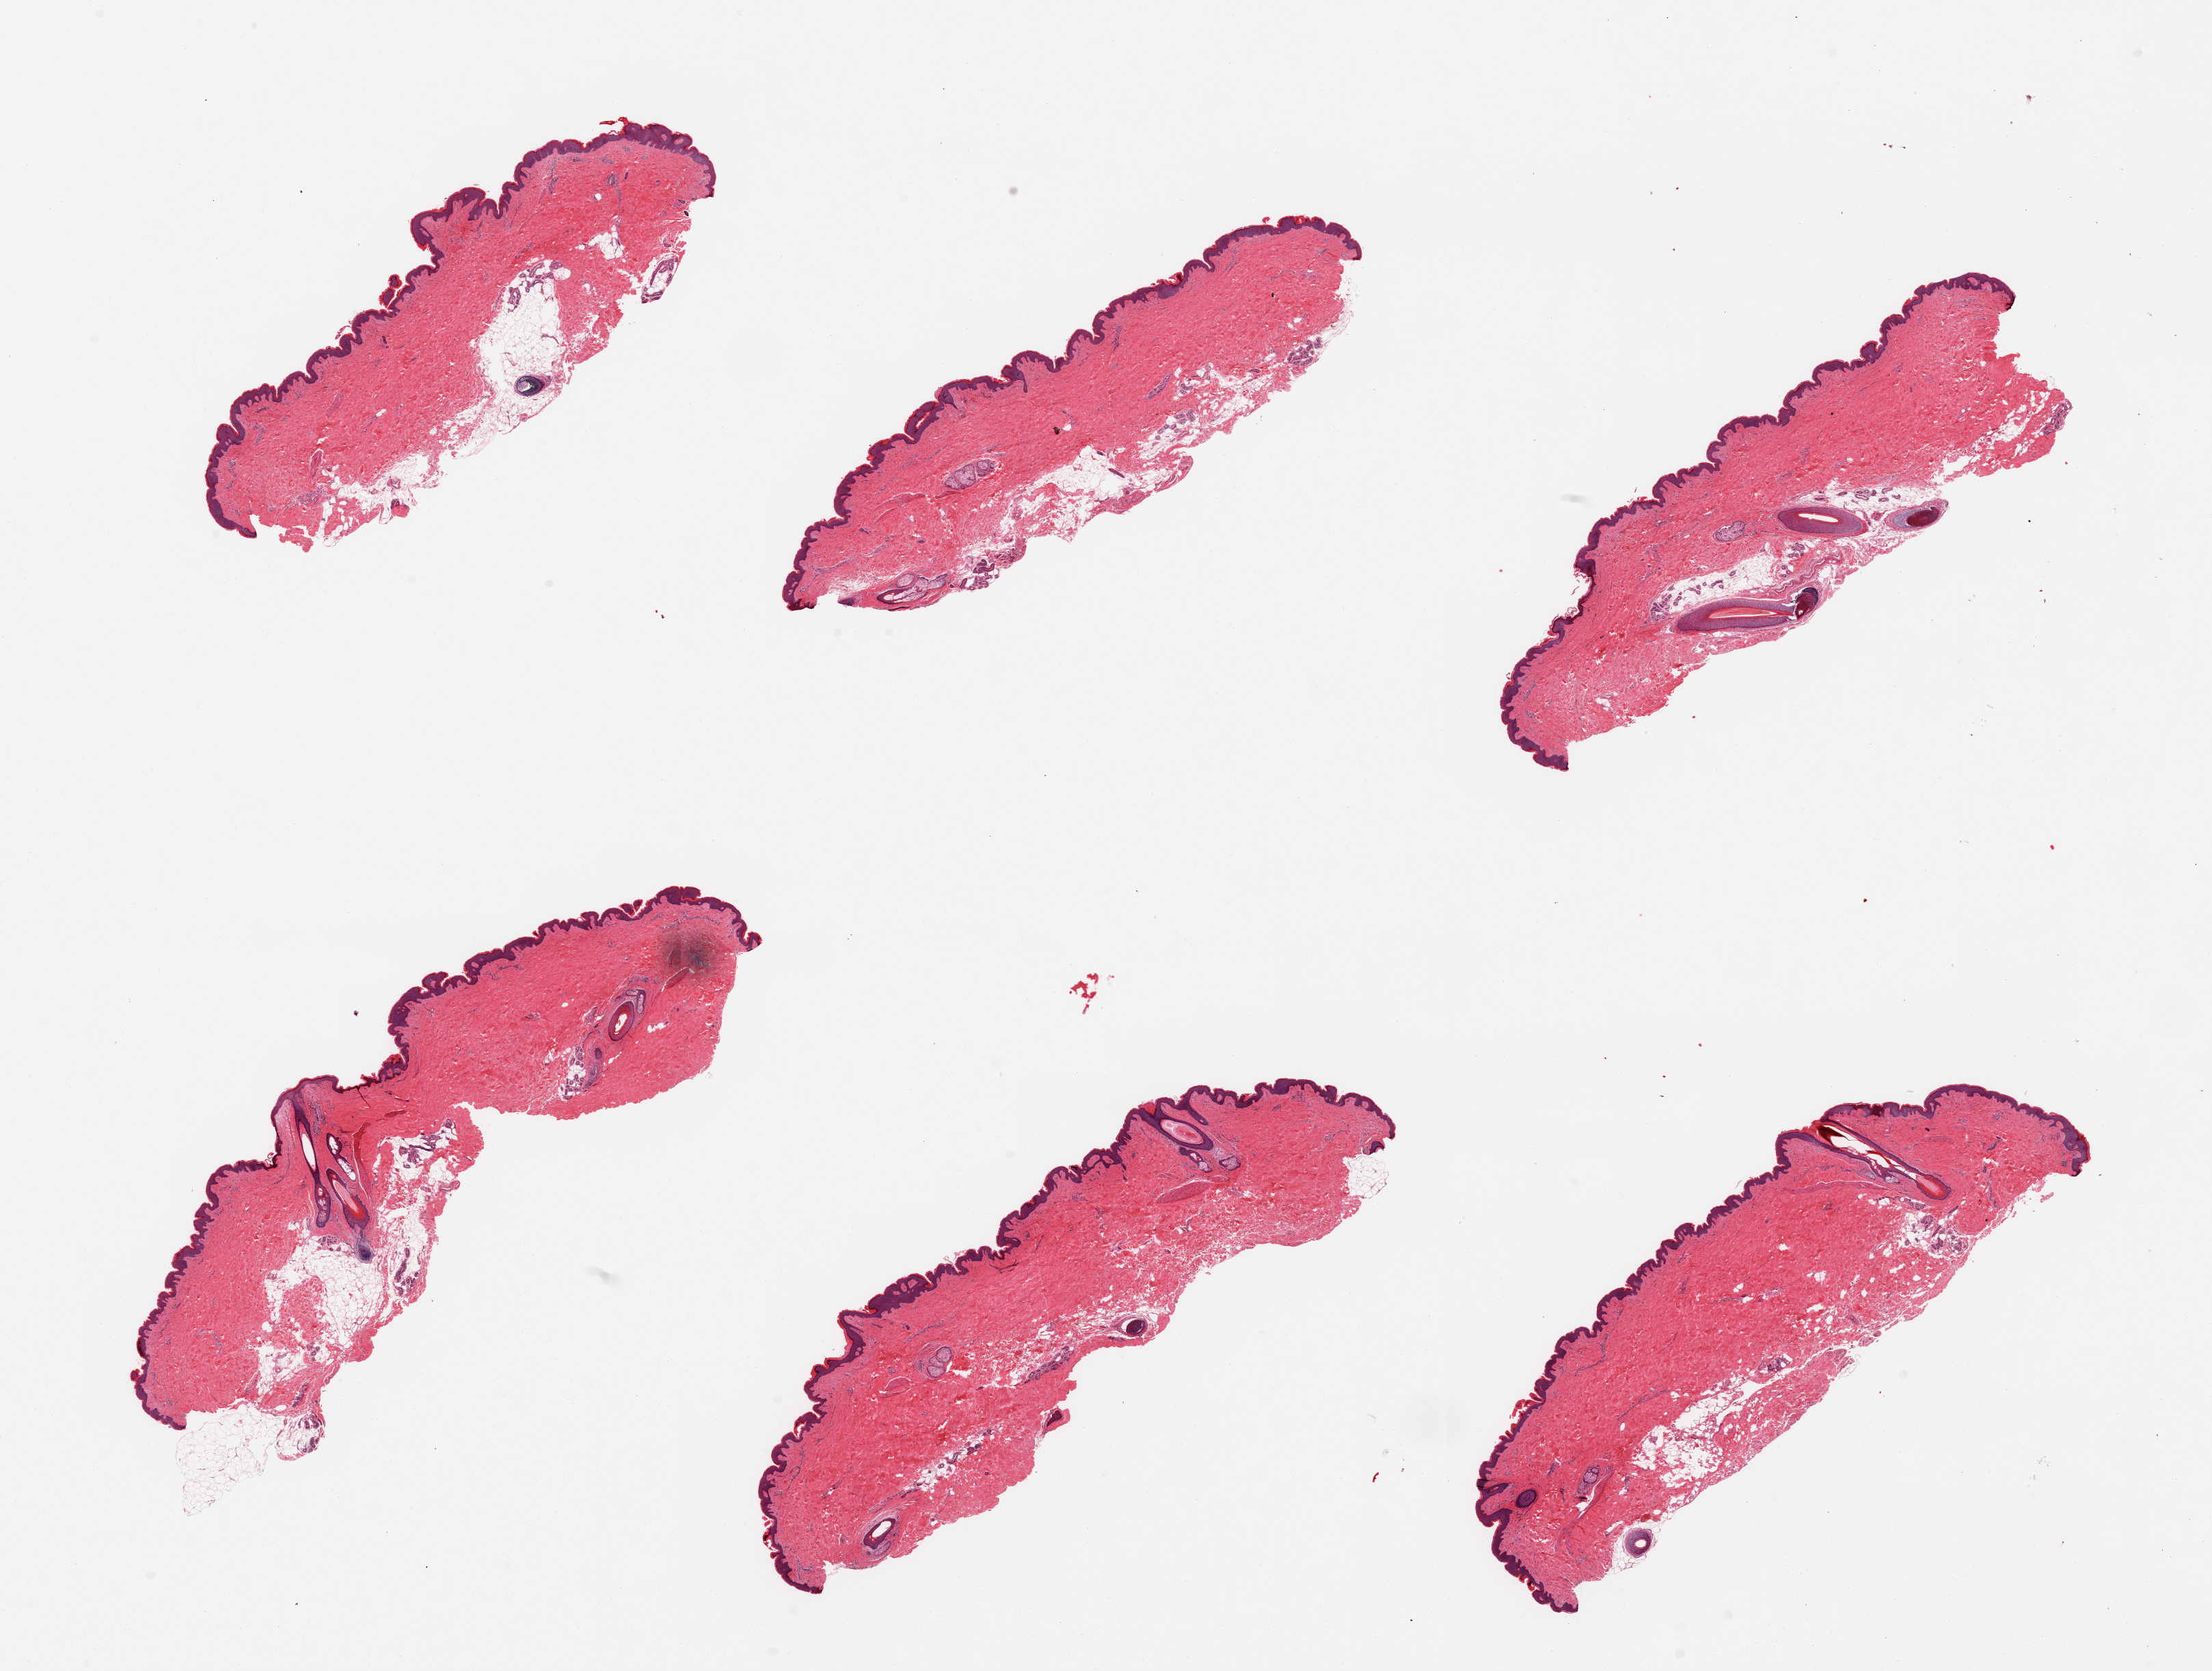
Whole-slide image, hematoxylin and eosin (H&E) stain, brightfield — low-resolution overview of the scanned area, about 25.6 x 19.3 mm; PAXgene-fixed, paraffin-embedded tissue; target tissue: skin of suprapubic region; tissue donor sample. Donor sex: female.
Review note (as recorded): 6 pieces, squamous epithelium is ~50-70 microns.